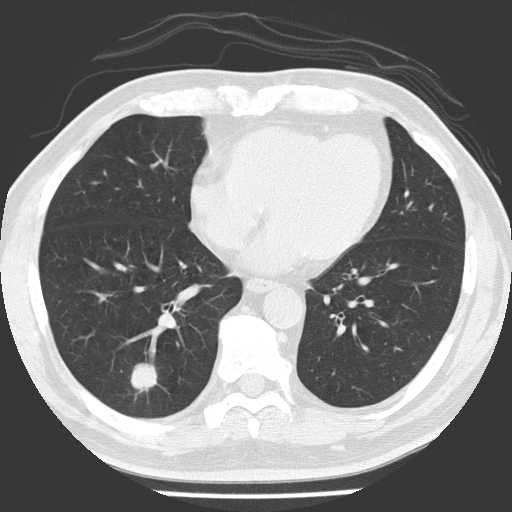
Low-dose screening chest CT, one axial slice. Position 62 of 154 along the scan axis. 120 kVp. Lung window (W 1500 / L -600 HU). 2 mm slice thickness. 512 × 512 image matrix, field of view 311 × 311 mm.
Annotated regions visible in this slice (expert manual segmentation):
- lesion 1 (tumor, lower lobe of right lung): bounding box (x1, y1, x2, y2) in pixels: (131, 363, 157, 392)